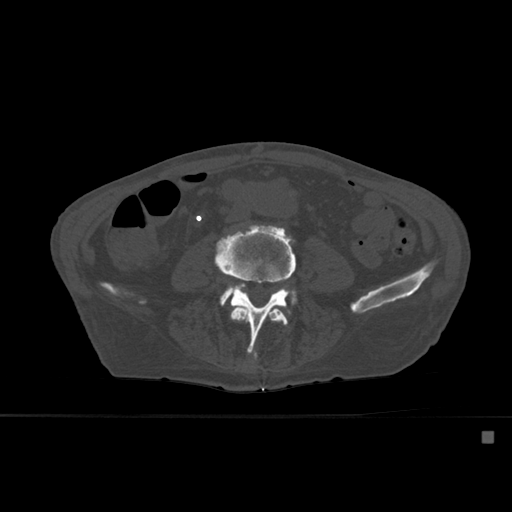
CT including the spine, one axial slice; slice 194 of 527 in the series (ordered by position); bone window (W 1800 / L 400 HU); 1.5 mm slice thickness; 512 × 512 image matrix. Patient: male, 78 years. From the clinical record (not read from this slice): primary cancer: prostate.
Outlined on this slice (semi-automatically segmented with operator editing):
- L3 vertebra: bounding box <230,307,288,364> (left, top, right, bottom; pixels)
- L4 vertebra: <215,227,298,358>
- L5 vertebra: <221,288,281,305>